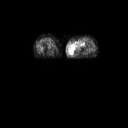
FDG PET of an extremity soft-tissue mass (from a PET/CT study), one axial slice; position 15 of 91 along the scan axis; 3.27 mm slice thickness; 128 × 128 image matrix. Female patient, age 74 years. From the clinical record (not read from this slice): histological type: pleomorphic leiomyosarcoma; grade: high; site of the primary tumour: left thigh.
Structures marked on this image (expert contour drawn on MRI and transferred to this co-registered scan by the dataset authors):
- gross tumour volume including surrounding oedema: box from (x=69, y=41) to (x=86, y=54) px
- gross tumour volume (mass): (x=69, y=47)–(x=76, y=54)